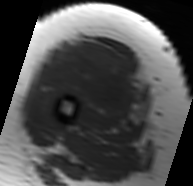
MRI of an extremity soft-tissue mass, one axial slice; slice 28 of 91 in the series (ordered by position); MR volume resampled by the dataset authors to the PET/CT grid (not the native acquisition matrix); 3.27 mm slice thickness; 193 × 186 image matrix, field of view 188 × 182 mm. Female patient. Case-level facts recorded for this patient, not image findings: histological type: malignant solitary fibrous tumor; grade: intermediate; site of the primary tumour: right thigh.
Structures marked on this image (expert contour drawn on MRI and transferred to this co-registered scan by the dataset authors):
- gross tumour volume including surrounding oedema: bounding box [x1, y1, x2, y2] px = [44, 39, 146, 123]
- gross tumour volume (mass): [47, 40, 141, 113]